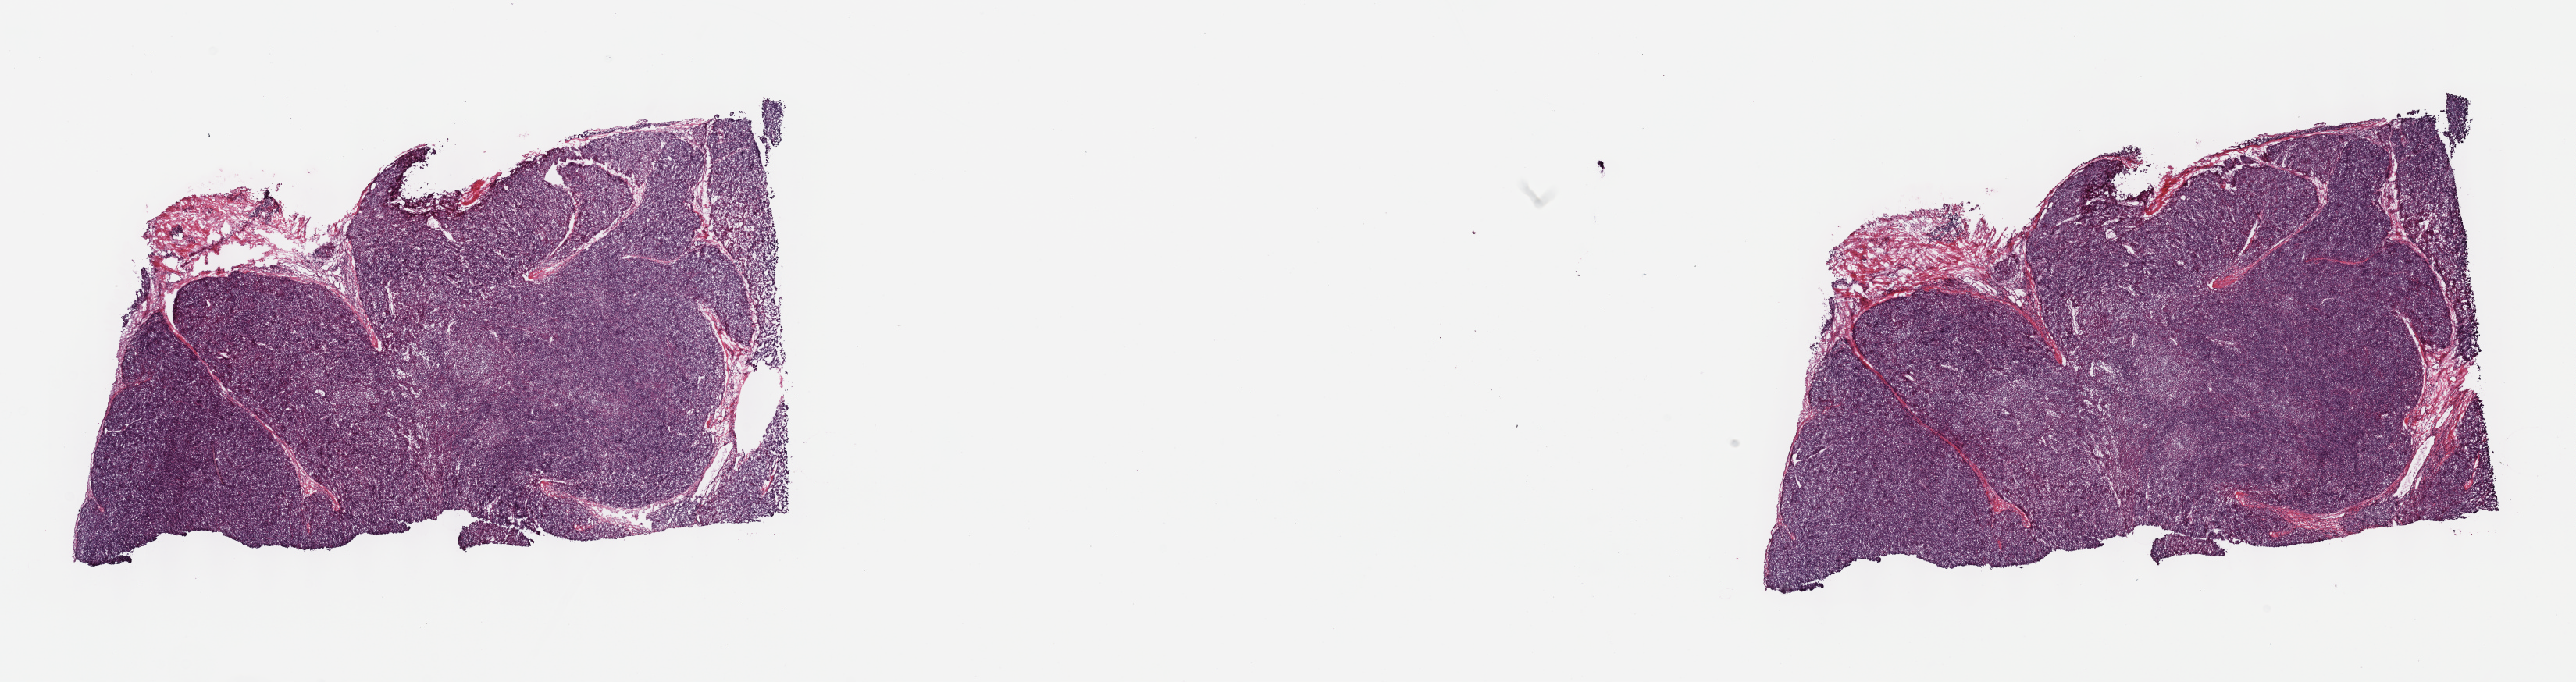
Digitized H&E-stained tissue section (whole slide) — low-resolution overview of the scanned area, about 26.7 x 7.1 mm (from a 40x scan). Frozen section. Thymus, primary tumour sample. Female, age 58 years at initial diagnosis. Composition of this section per pathologist review: tumour cells 80%, tumour nuclei 80%, normal cells 0%, stromal cells 20%, necrosis 0%. Infiltration values recorded for this section: lymphocyte infiltration 3%, monocyte infiltration 1%, neutrophil infiltration 1%.
Histologic diagnosis: Thymoma, type AB, malignant (anterior mediastinum).